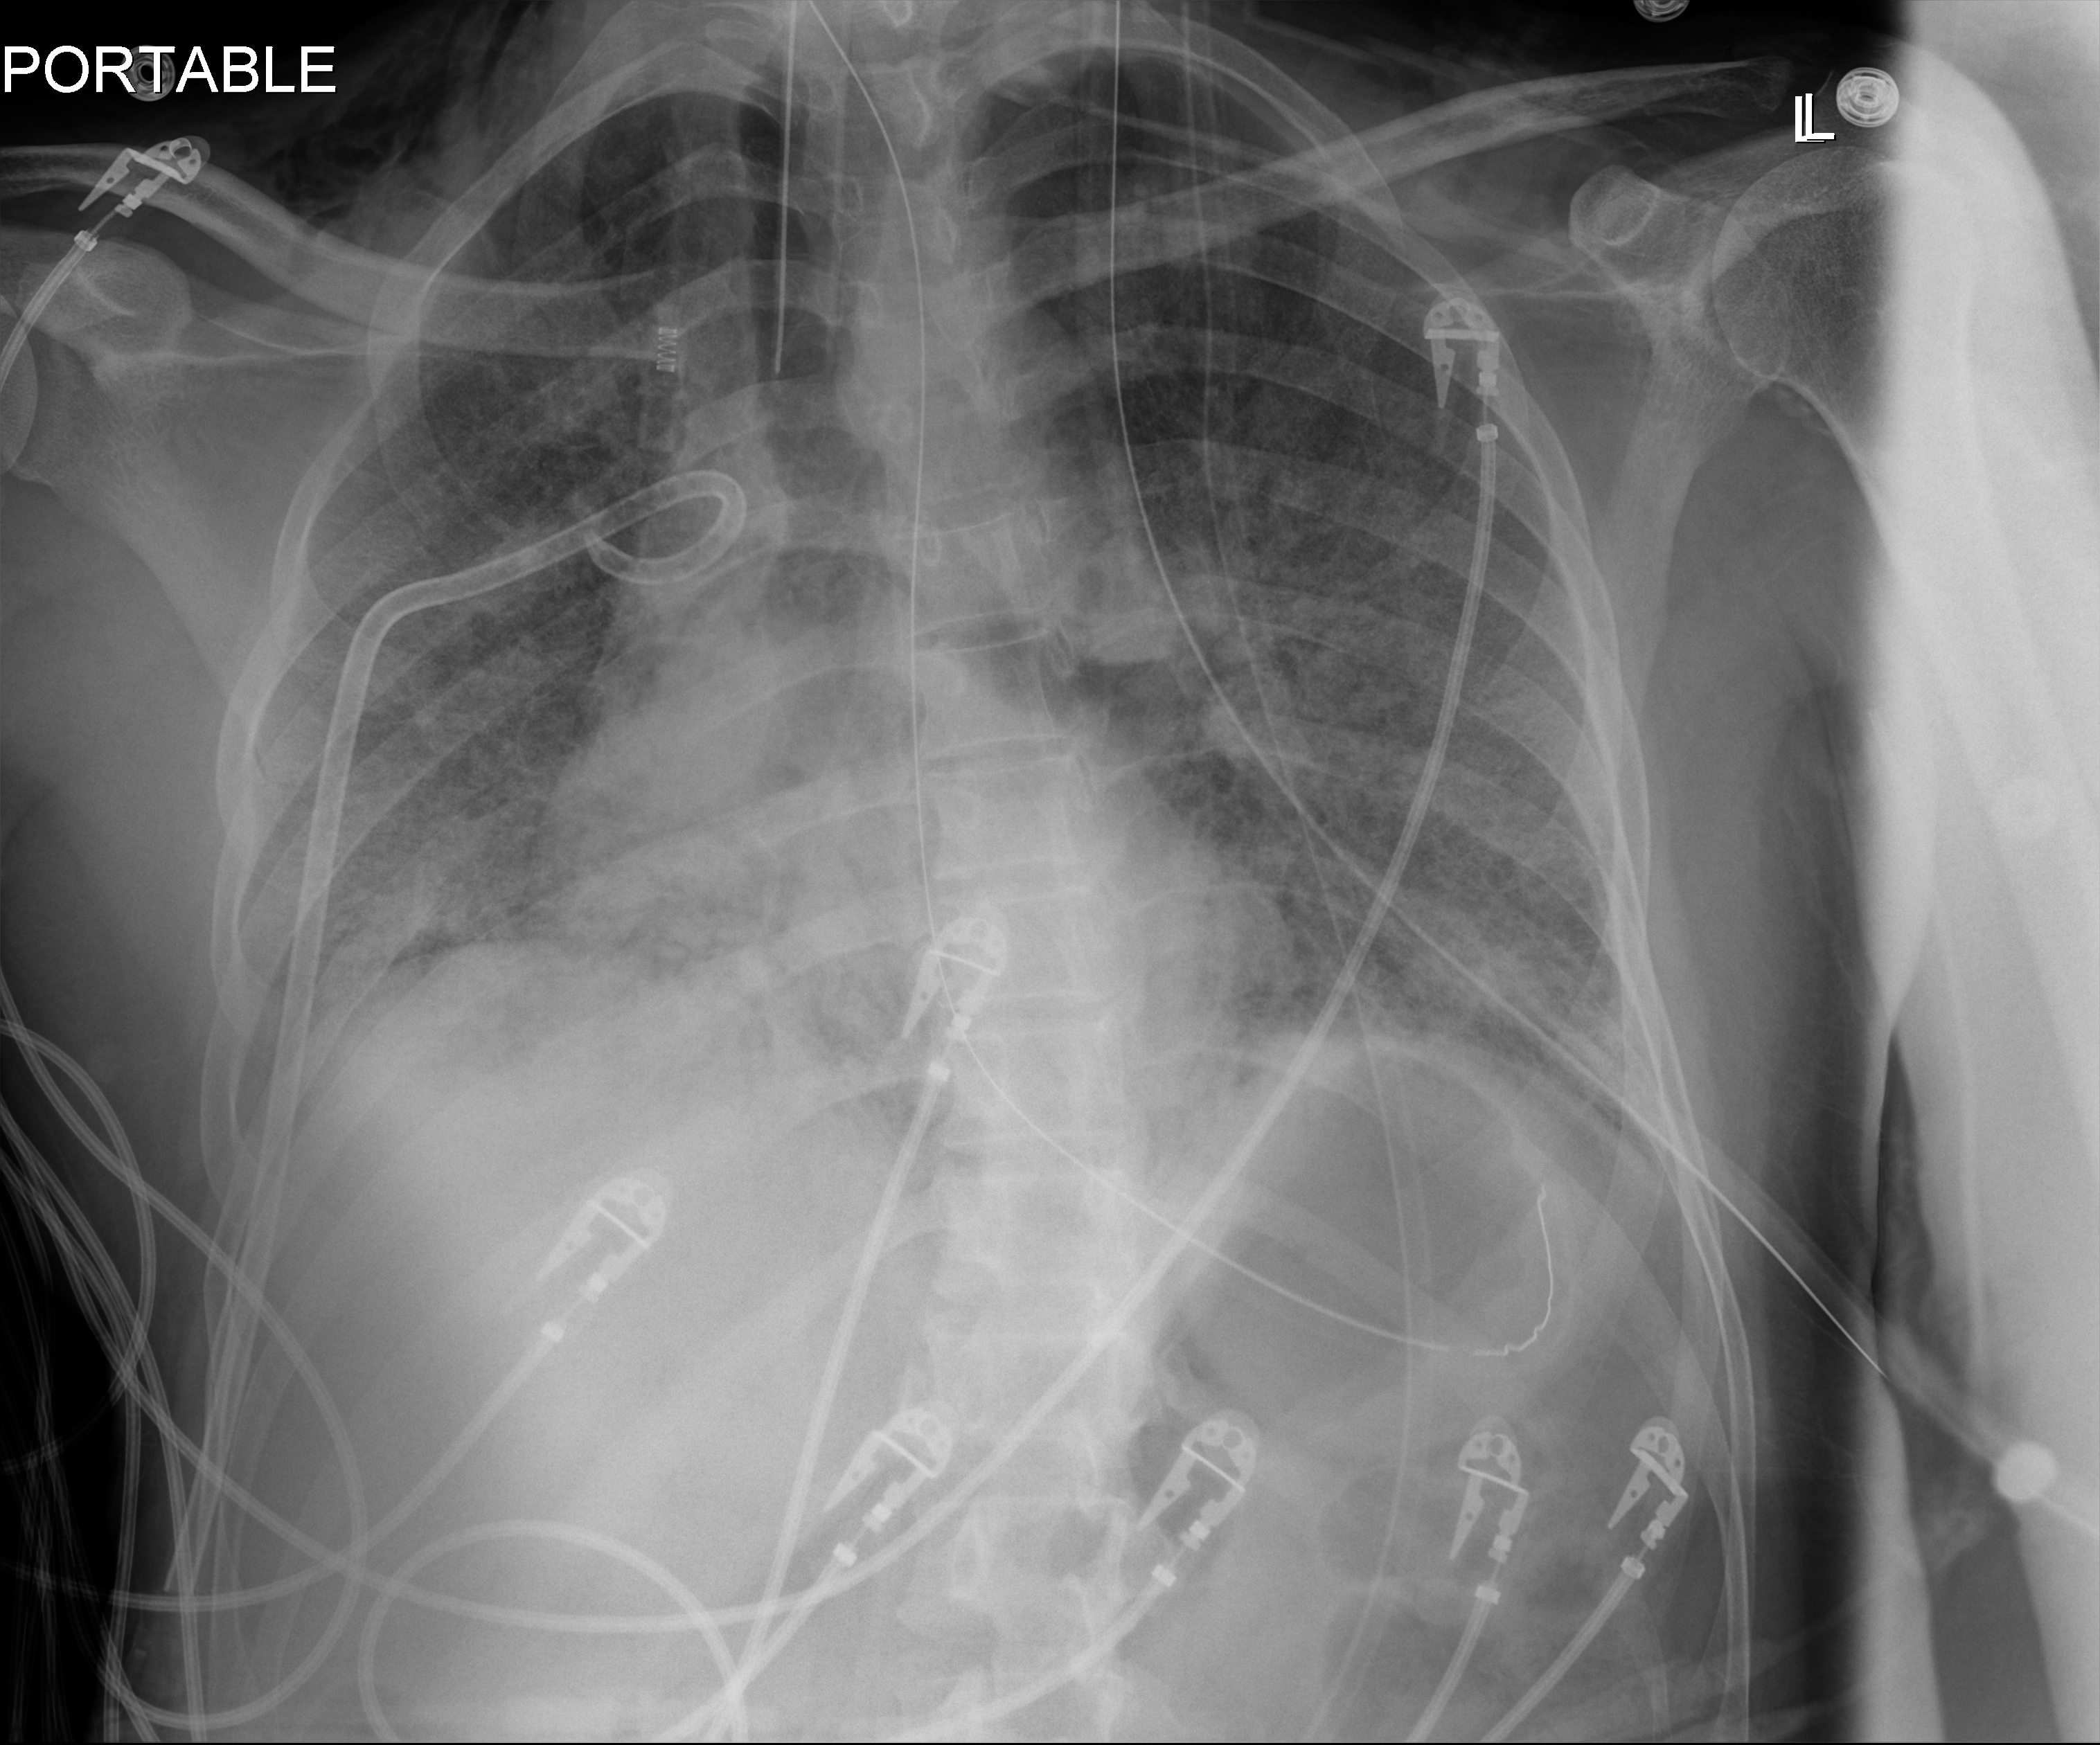
Chest X-ray (portable), anteroposterior (AP) projection. Adult patient hospitalised with COVID-19, age 18–59 years.
From the hospital-stay record, not from the radiograph (when in the stay this image was taken is not recorded): admitted to intensive care during this hospital stay: yes; length of hospital stay: 41 days.